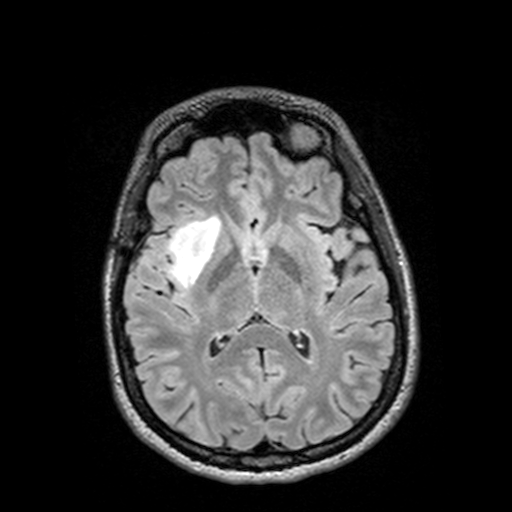
Brain MRI from a brain-tumour surgery series, one axial slice. Slice 68 of 144 in the series (ordered by position). T2 FLAIR. 1 mm slice thickness. 512 × 512 image matrix. From the clinical record (not read from this slice): histopathology: Astrocytoma; WHO grade: 3; IDH mutation: yes; tumour location: Right Insular Temporal.
Structures marked on this image (outlined manually by an expert reader):
- tumour: bounding box [x1, y1, x2, y2] px = [126, 215, 232, 288]